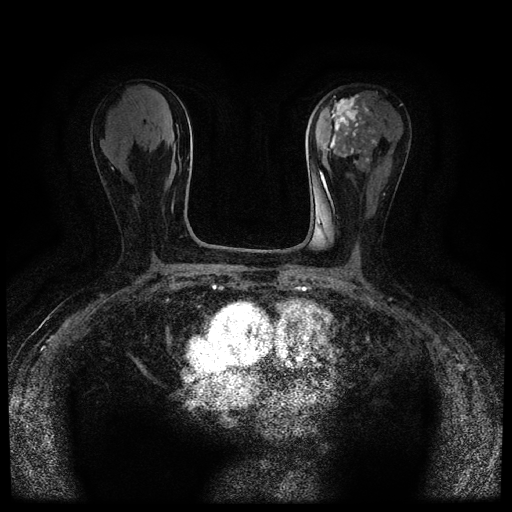
Breast MRI (dynamic contrast-enhanced, multi-phase), one axial slice. Position 41 of 116 along the scan axis. Dynamic contrast-enhanced series, time point 2 of 5 at this slice position (early post-contrast). 1.5 T. TE 2.7 ms, TR 5.4 ms. 2 mm slice thickness. 512 × 512 image matrix. Female patient, age 80 years.
Structures marked on this image (semi-automatically segmented with operator editing):
- breast lesion (labelled 'tumour' in the annotation; benign lesions carry a separate 'benign' label): bounding box <323,95,377,165> (left, top, right, bottom; pixels)